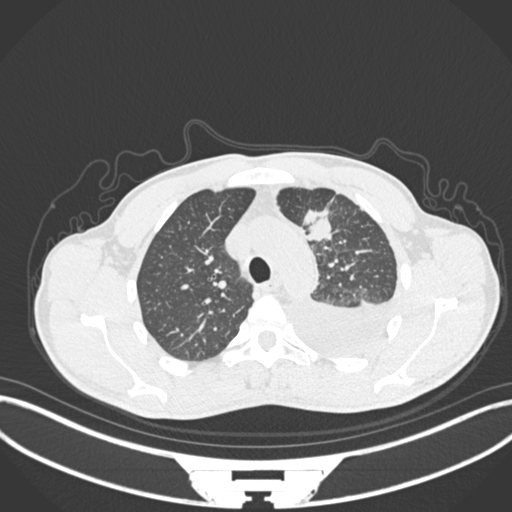
Chest CT, one axial slice. Position 165 of 244 along the scan axis. Reconstruction kernel B30f. Lung window (W 1500 / L -600 HU). 1 mm slice thickness. 512 × 512 image matrix. Male patient, age 49 years. From the clinical record (not read from this slice): clinical TNM (as recorded): T1c N1 M1.
Structures marked on this image (bounding box drawn by a radiologist):
- lung tumour (recorded histology: adenocarcinoma): box from (x=301, y=202) to (x=342, y=250) px